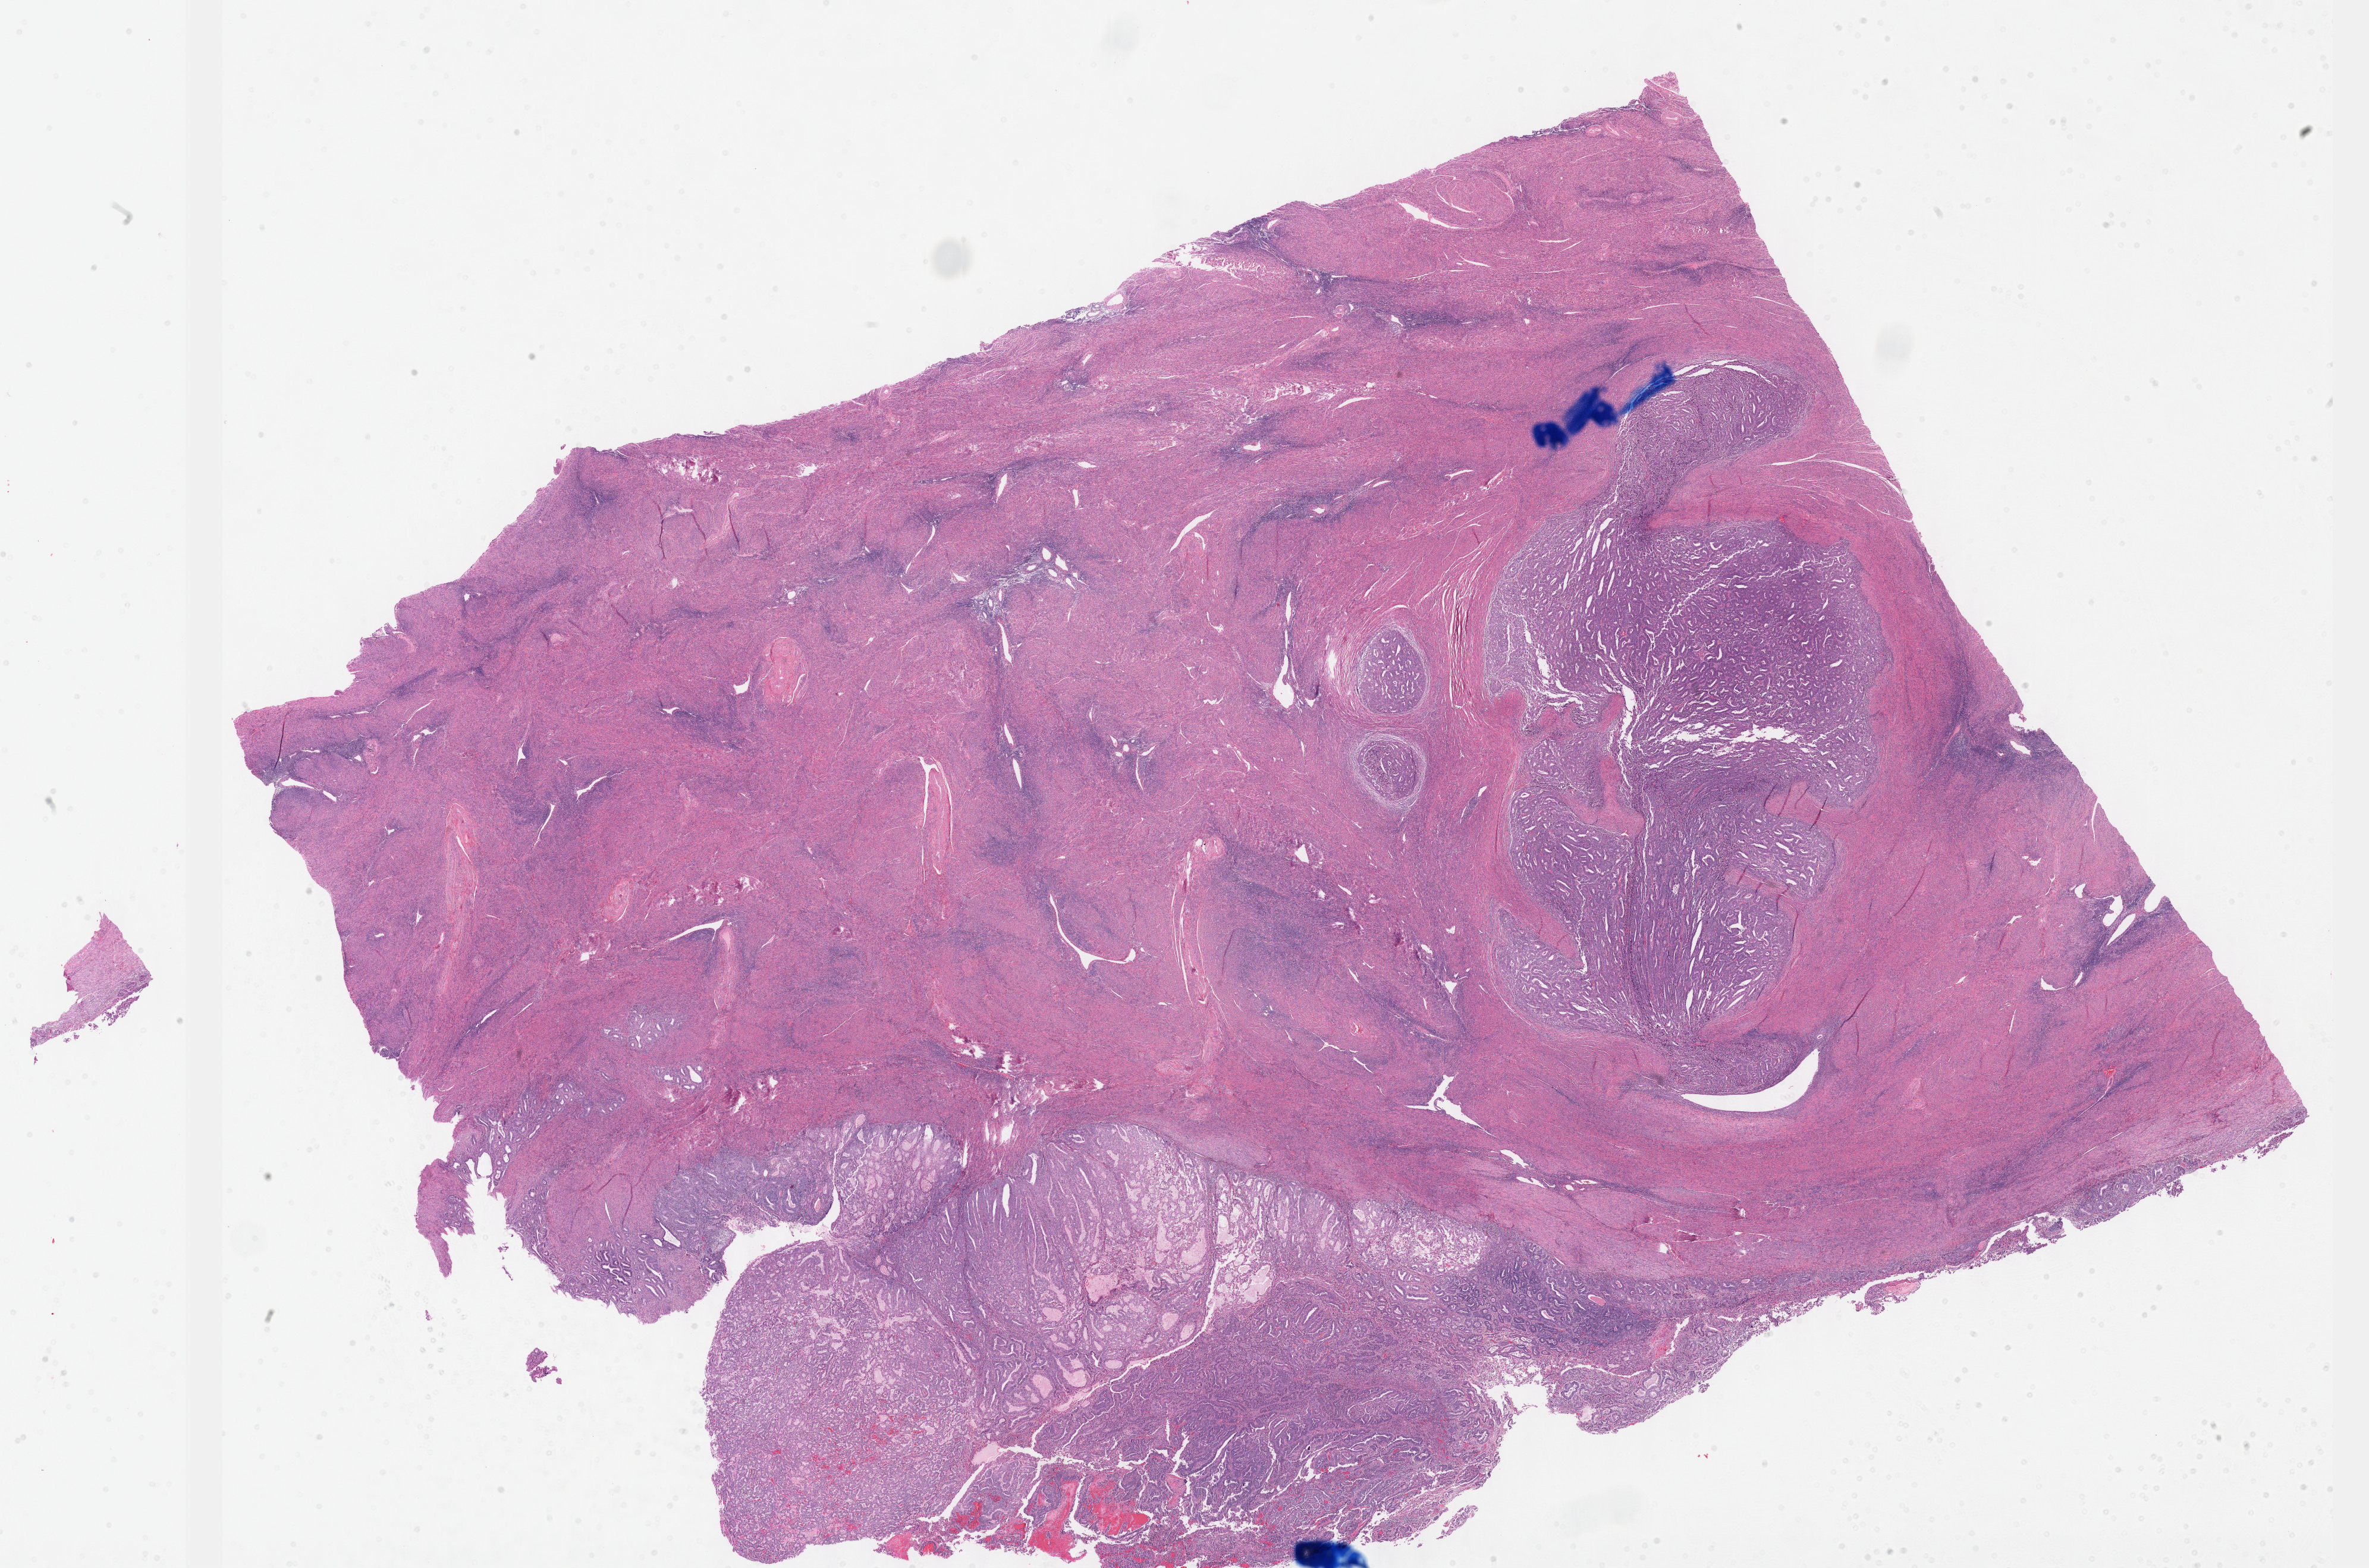
Whole-slide histology image, Hematoxylin and eosin (H&E) stained, a low-resolution overview of the entire scanned area, about 32.2 x 21.3 mm (from a 40x scan); formalin-fixed paraffin-embedded (FFPE) diagnostic section; sample: primary tumour, uterus. Female patient; age at initial diagnosis 74 years. Histologic grade: G2 (moderately differentiated).
- diagnosis: Endometrioid adenocarcinoma, NOS
- FIGO stage: IA